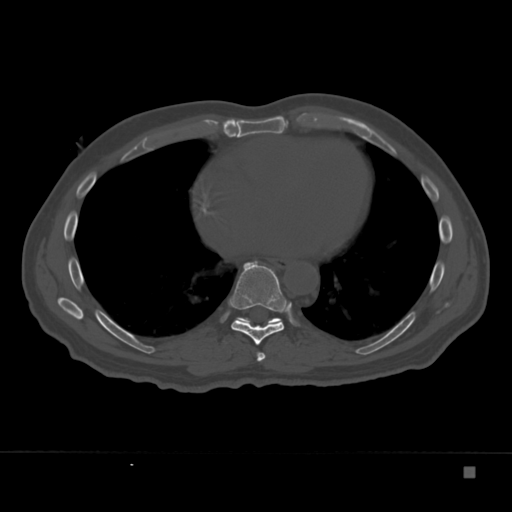
CT including the spine, one axial slice; slice 204 of 332 in the series (ordered by position); bone window (W 1800 / L 400 HU); 1.5 mm slice thickness; 512 × 512 image matrix, field of view 389 × 389 mm. Patient: male, 72 years. From the clinical record (not read from this slice): primary cancer: skeletal.
Outlined on this slice (semi-automatically segmented with operator editing):
- T7 vertebra: box from (x=257, y=352) to (x=266, y=362) px
- T8 vertebra: (x=229, y=261)–(x=289, y=345)
- T9 vertebra: (x=237, y=317)–(x=283, y=325)